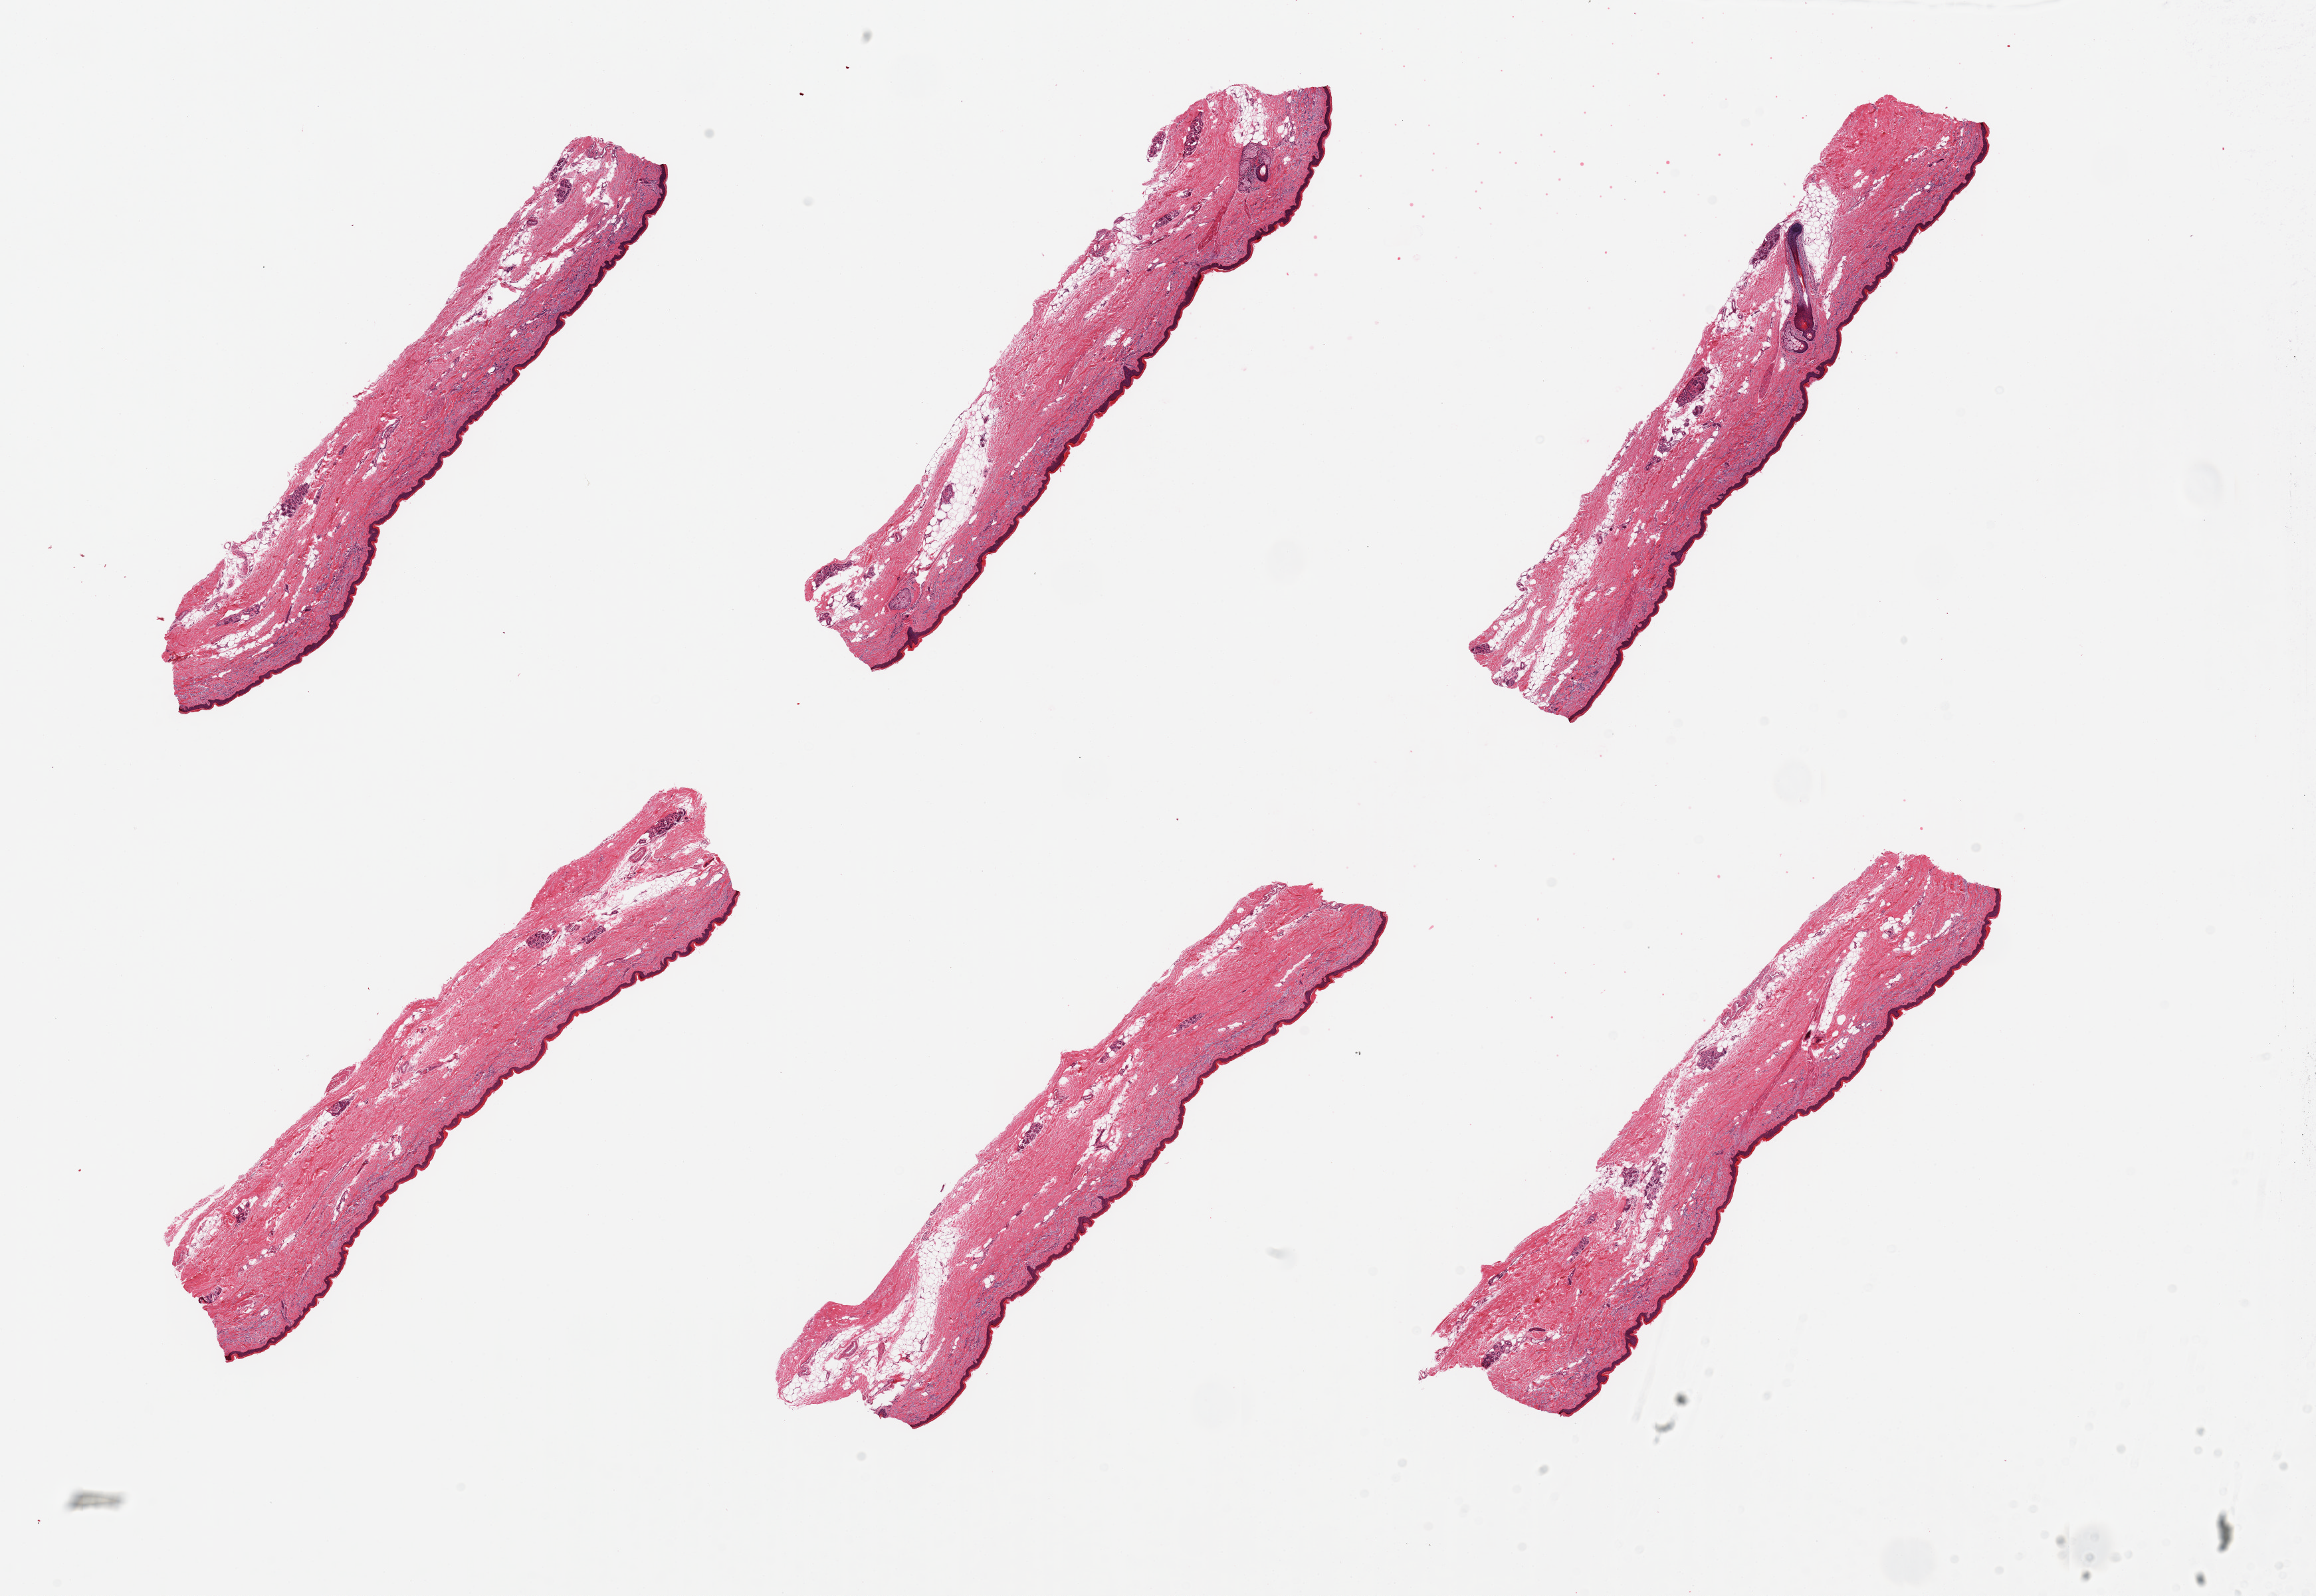
Digitized haematoxylin and eosin-stained section — shown as a low-resolution overview of the whole scanned area (about 27.6 x 19.0 mm, from a 20x scan); PAXgene-fixed, paraffin-embedded tissue; sampled site (target tissue): skin of lower leg; donor tissue sample. Male donor.
Review note (as recorded): 6 pieces, minimal dermal fat. Squamous epithelium is ~50microns. Moderate solar elastosis in upper dermis.